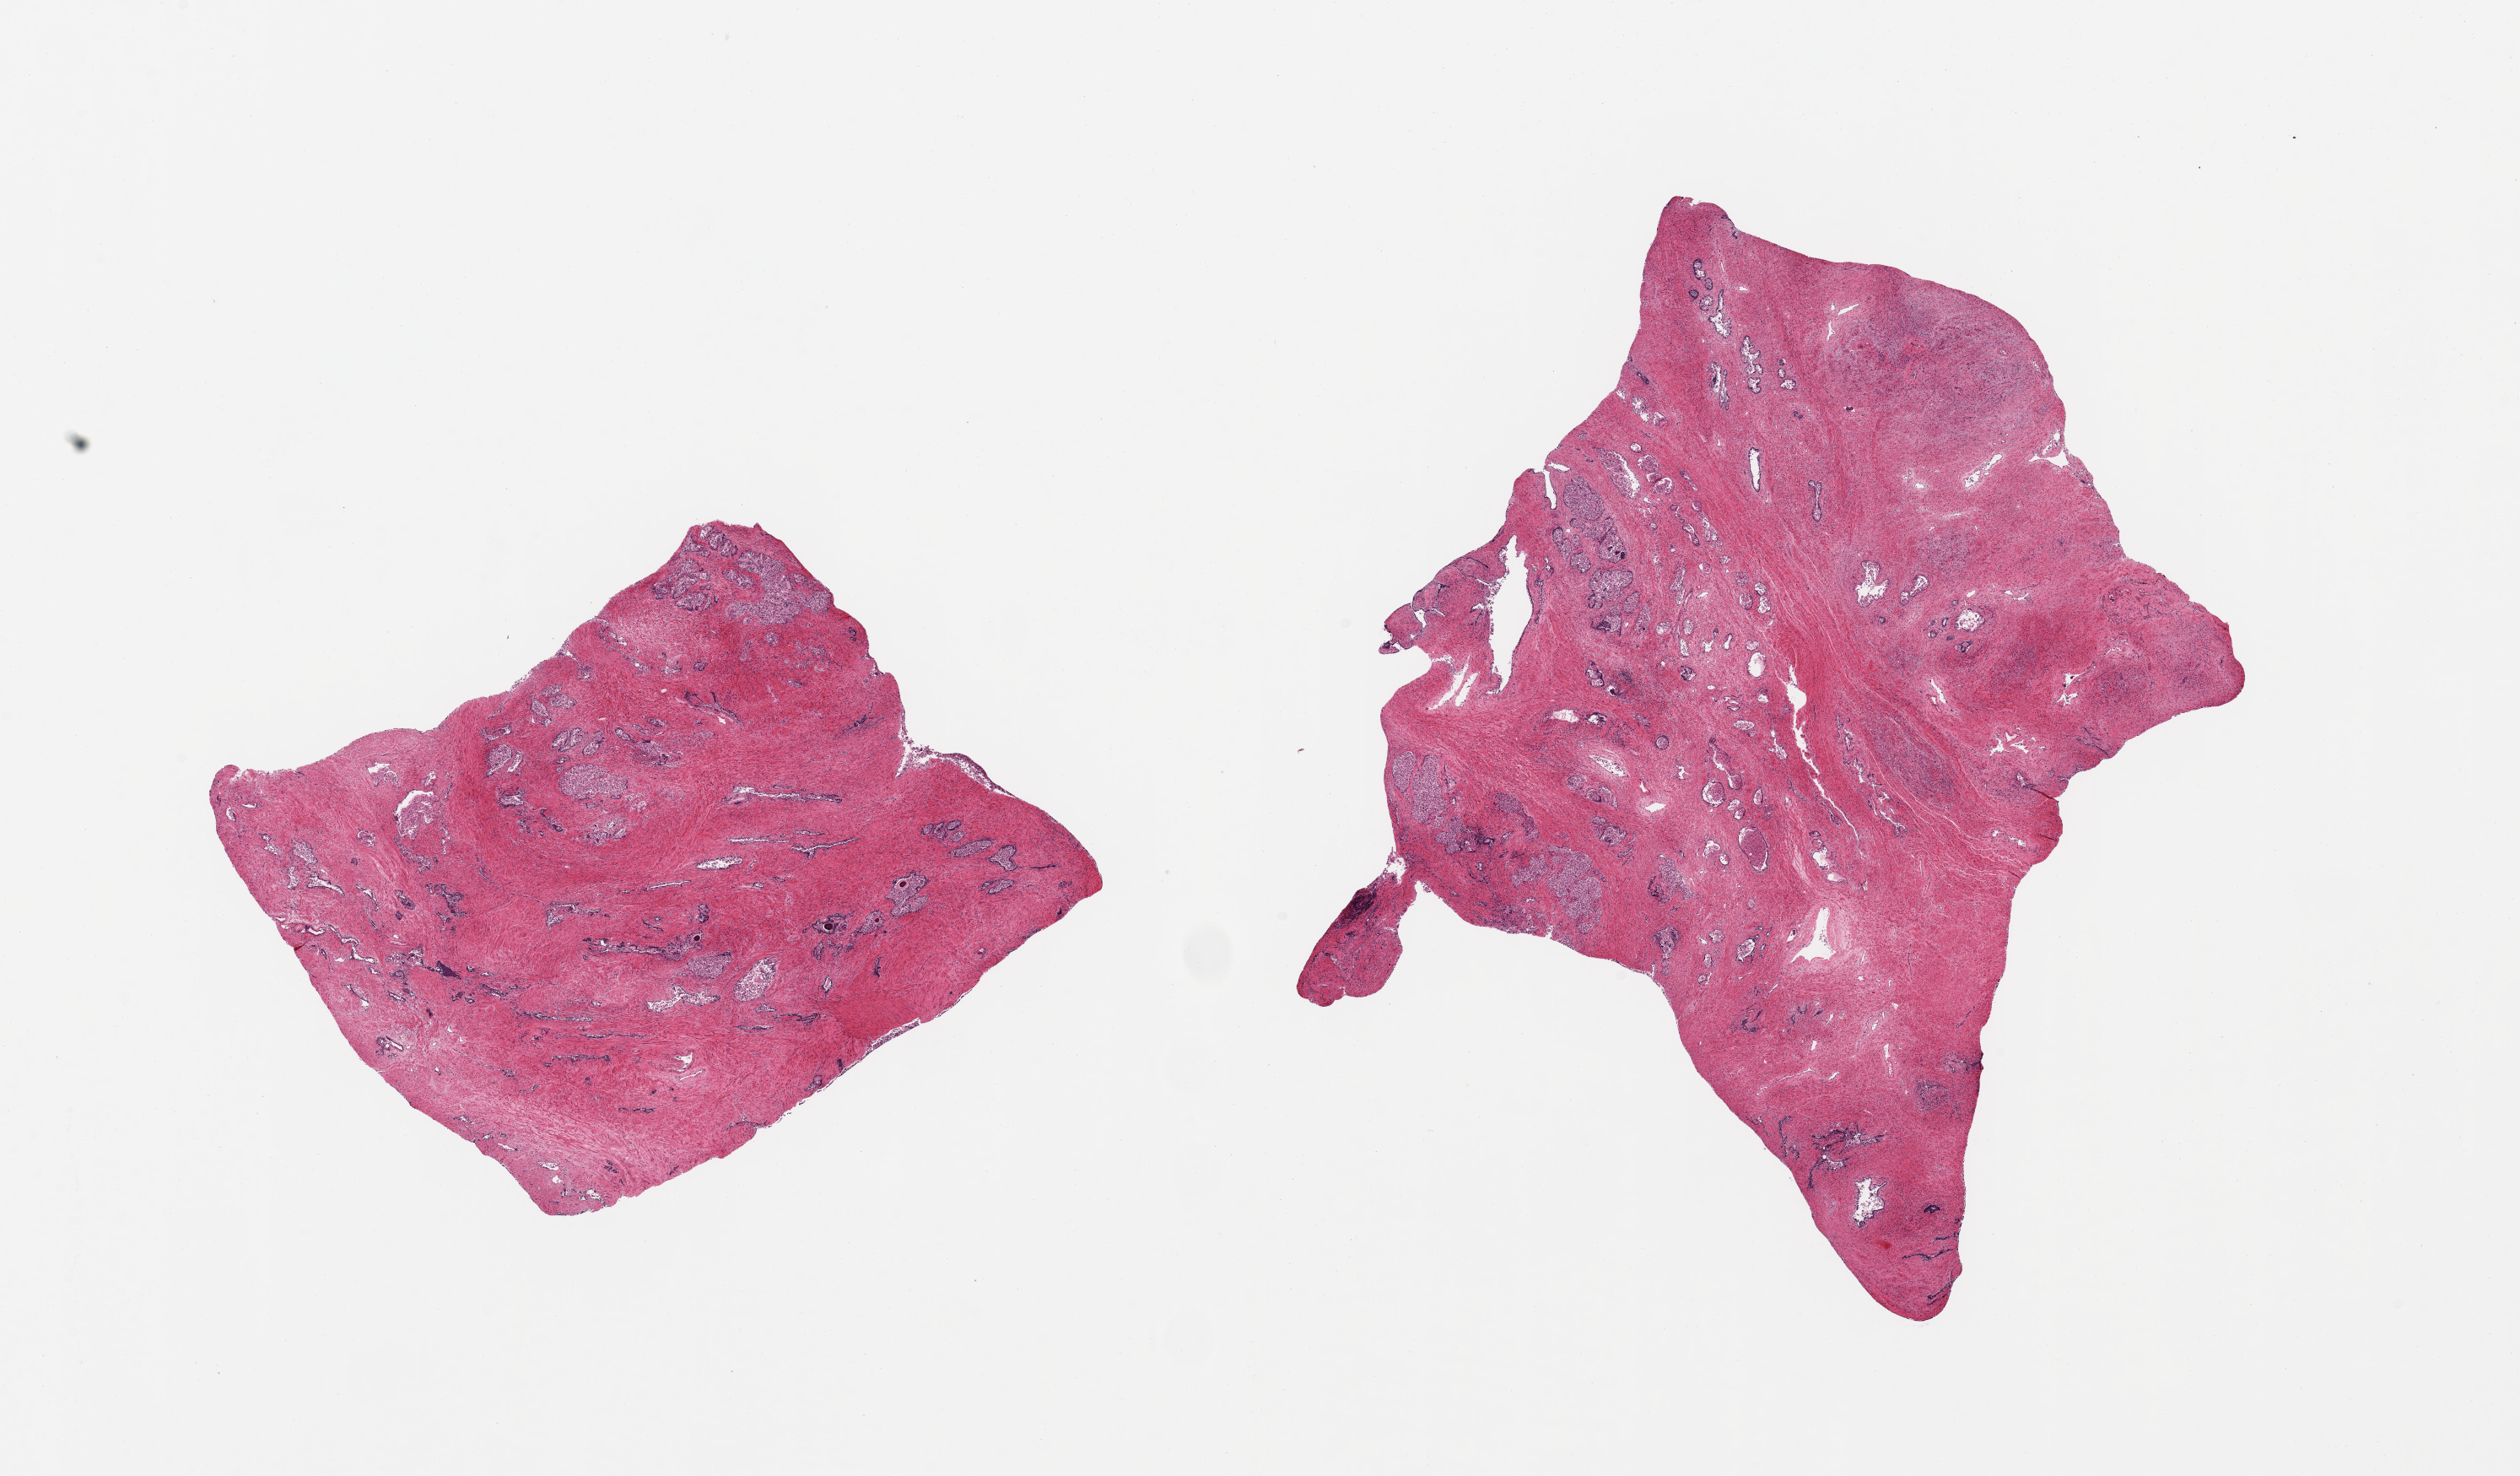
Haematoxylin and eosin whole-slide image — shown as a low-resolution overview of the whole scanned area (about 23.6 x 13.8 mm); PAXgene-fixed, paraffin-embedded tissue; target tissue: prostate; tissue donor sample. Donor sex: male.
Review note (as recorded): 2 pieces; moderate to severe autolysis, fibromuscular stroma and glandular component with sloughed lining epithelium.